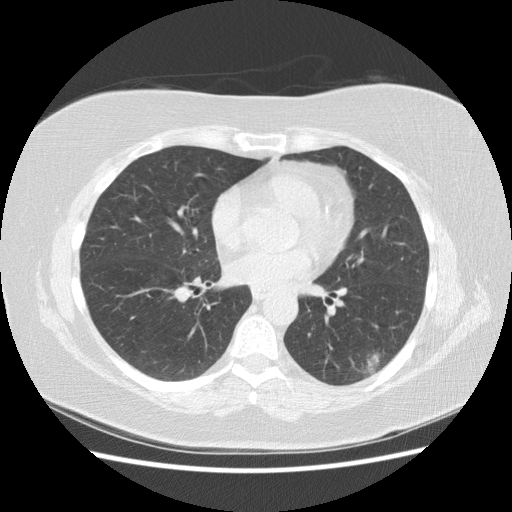
Low-dose screening chest CT, one axial slice. Slice 73 of 151 in the series (ordered by position). Lung window (W 1500 / L -600 HU). 2.5 mm slice thickness. 512 × 512 image matrix, field of view 360 × 360 mm.
Structures marked on this image (expert manual segmentation):
- lesion 1 (tumor, lower lobe of left lung): bounding box <366,353,384,375> (left, top, right, bottom; pixels)